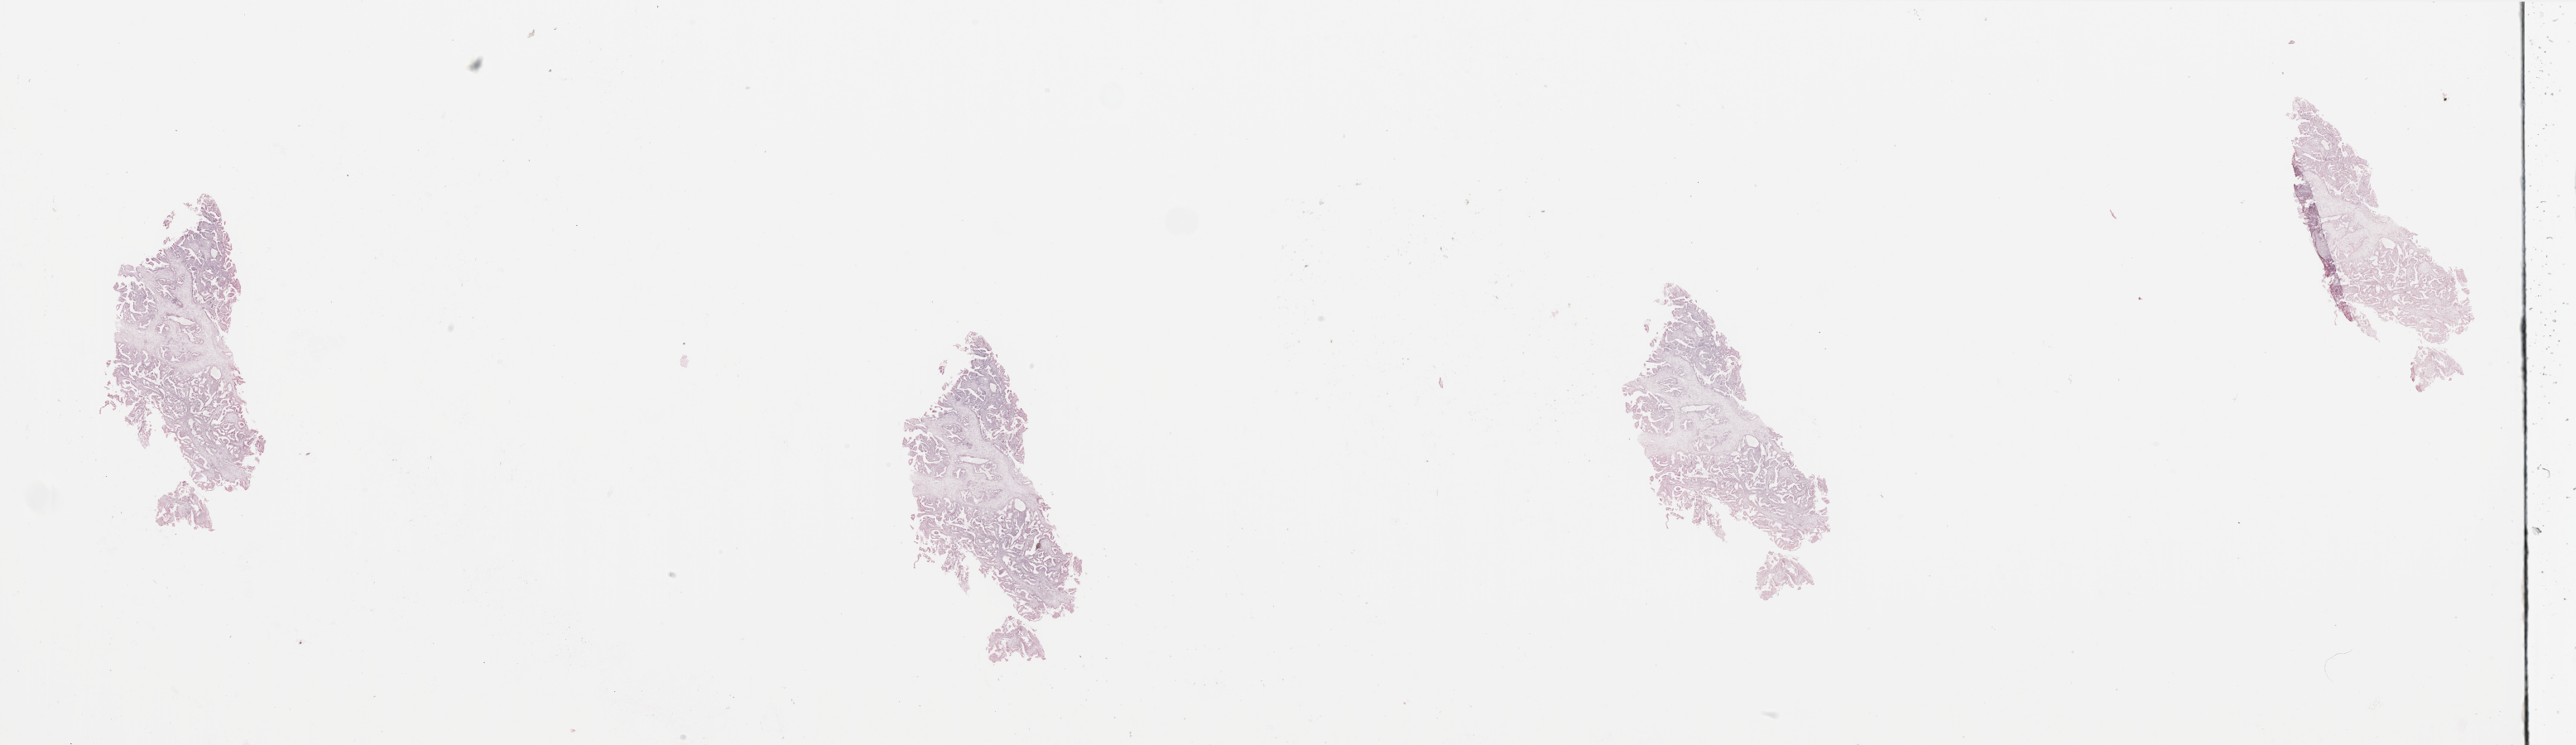
H&E whole-slide image — a low-resolution overview of the entire scanned area, about 49.2 x 14.2 mm. Tumour tissue sample, sampled site: uterus. Female, 58 y/o. Histologic grade: G1 (well differentiated). Composition of this section per pathologist review: tumour nuclei 80%, necrosis 0%.
* diagnosis: Endometrioid adenocarcinoma, NOS
* AJCC pathologic stage: III
* primary tumour site (as recorded): posterior endometrium